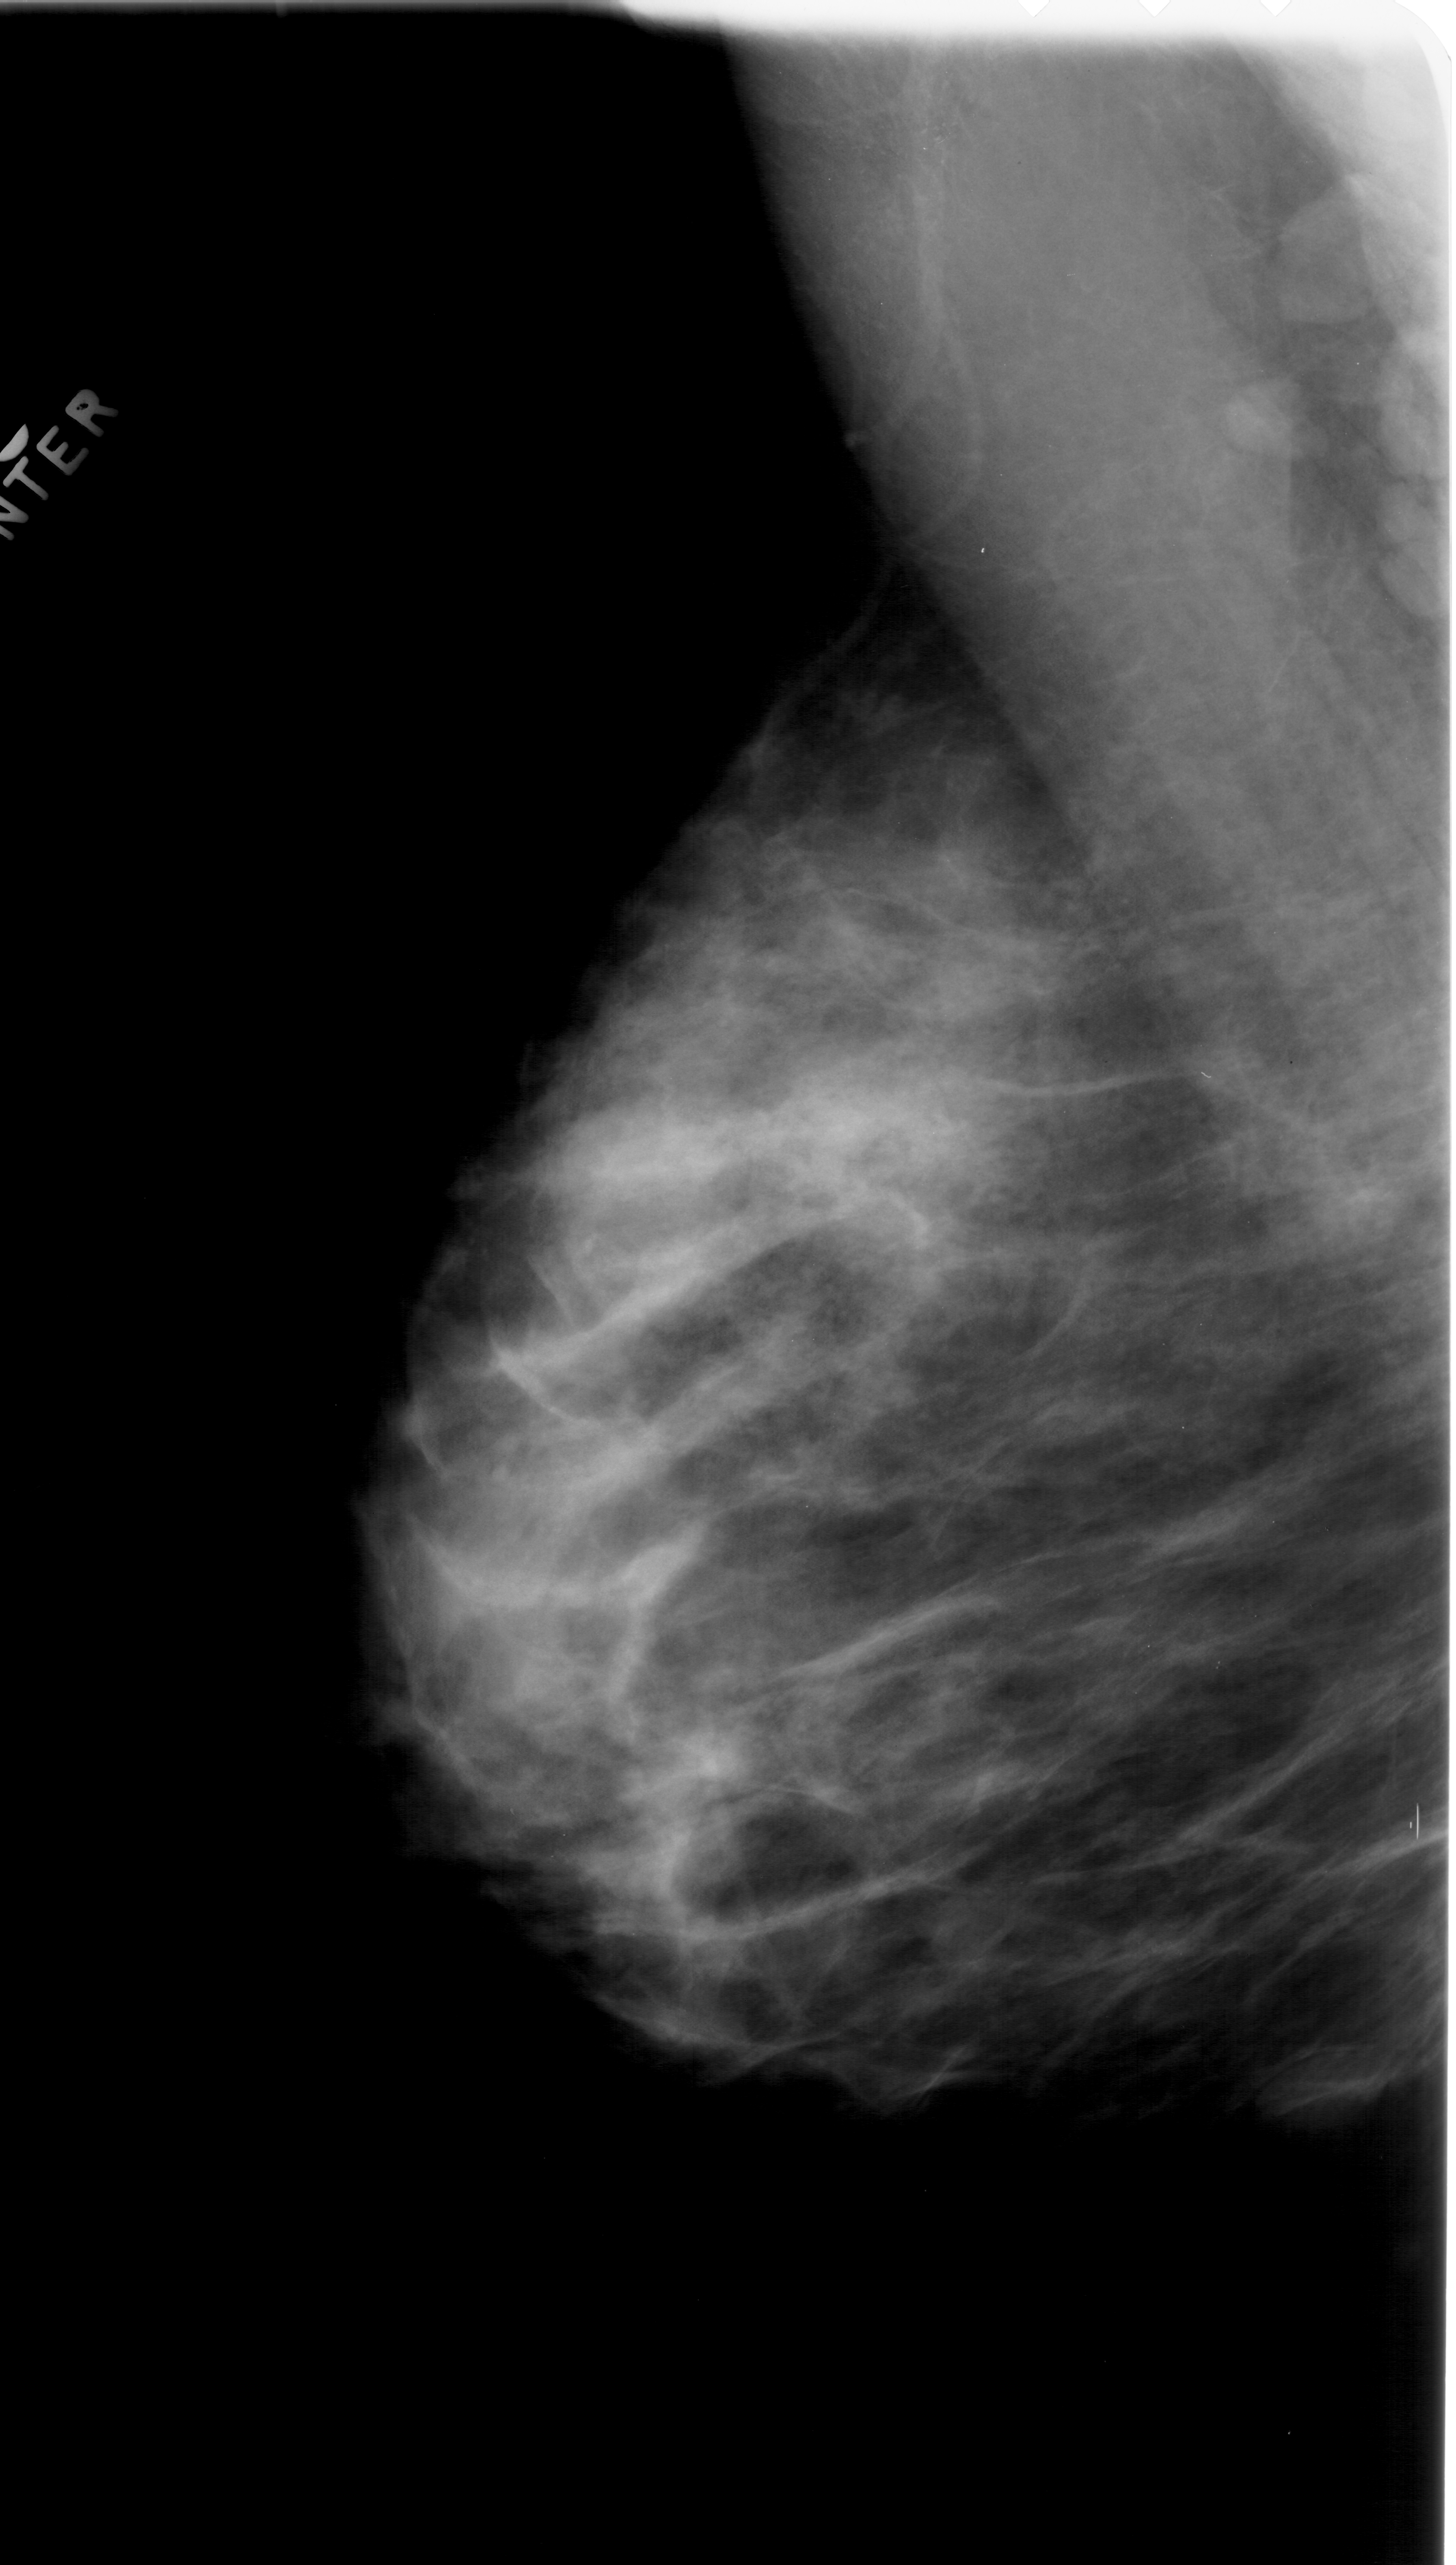
Digitized screen-film mammogram; left breast; MLO view; breast composition: extremely dense (BI-RADS density category 4 of 4); 1456 × 2565 image matrix.
Marked abnormalities (boxes around the expert regions of interest):
- mass, shape oval, margins circumscribed; BI-RADS assessment category 3; pathology (as recorded): benign: bounding box [x1, y1, x2, y2] px = [1250, 2040, 1412, 2139]